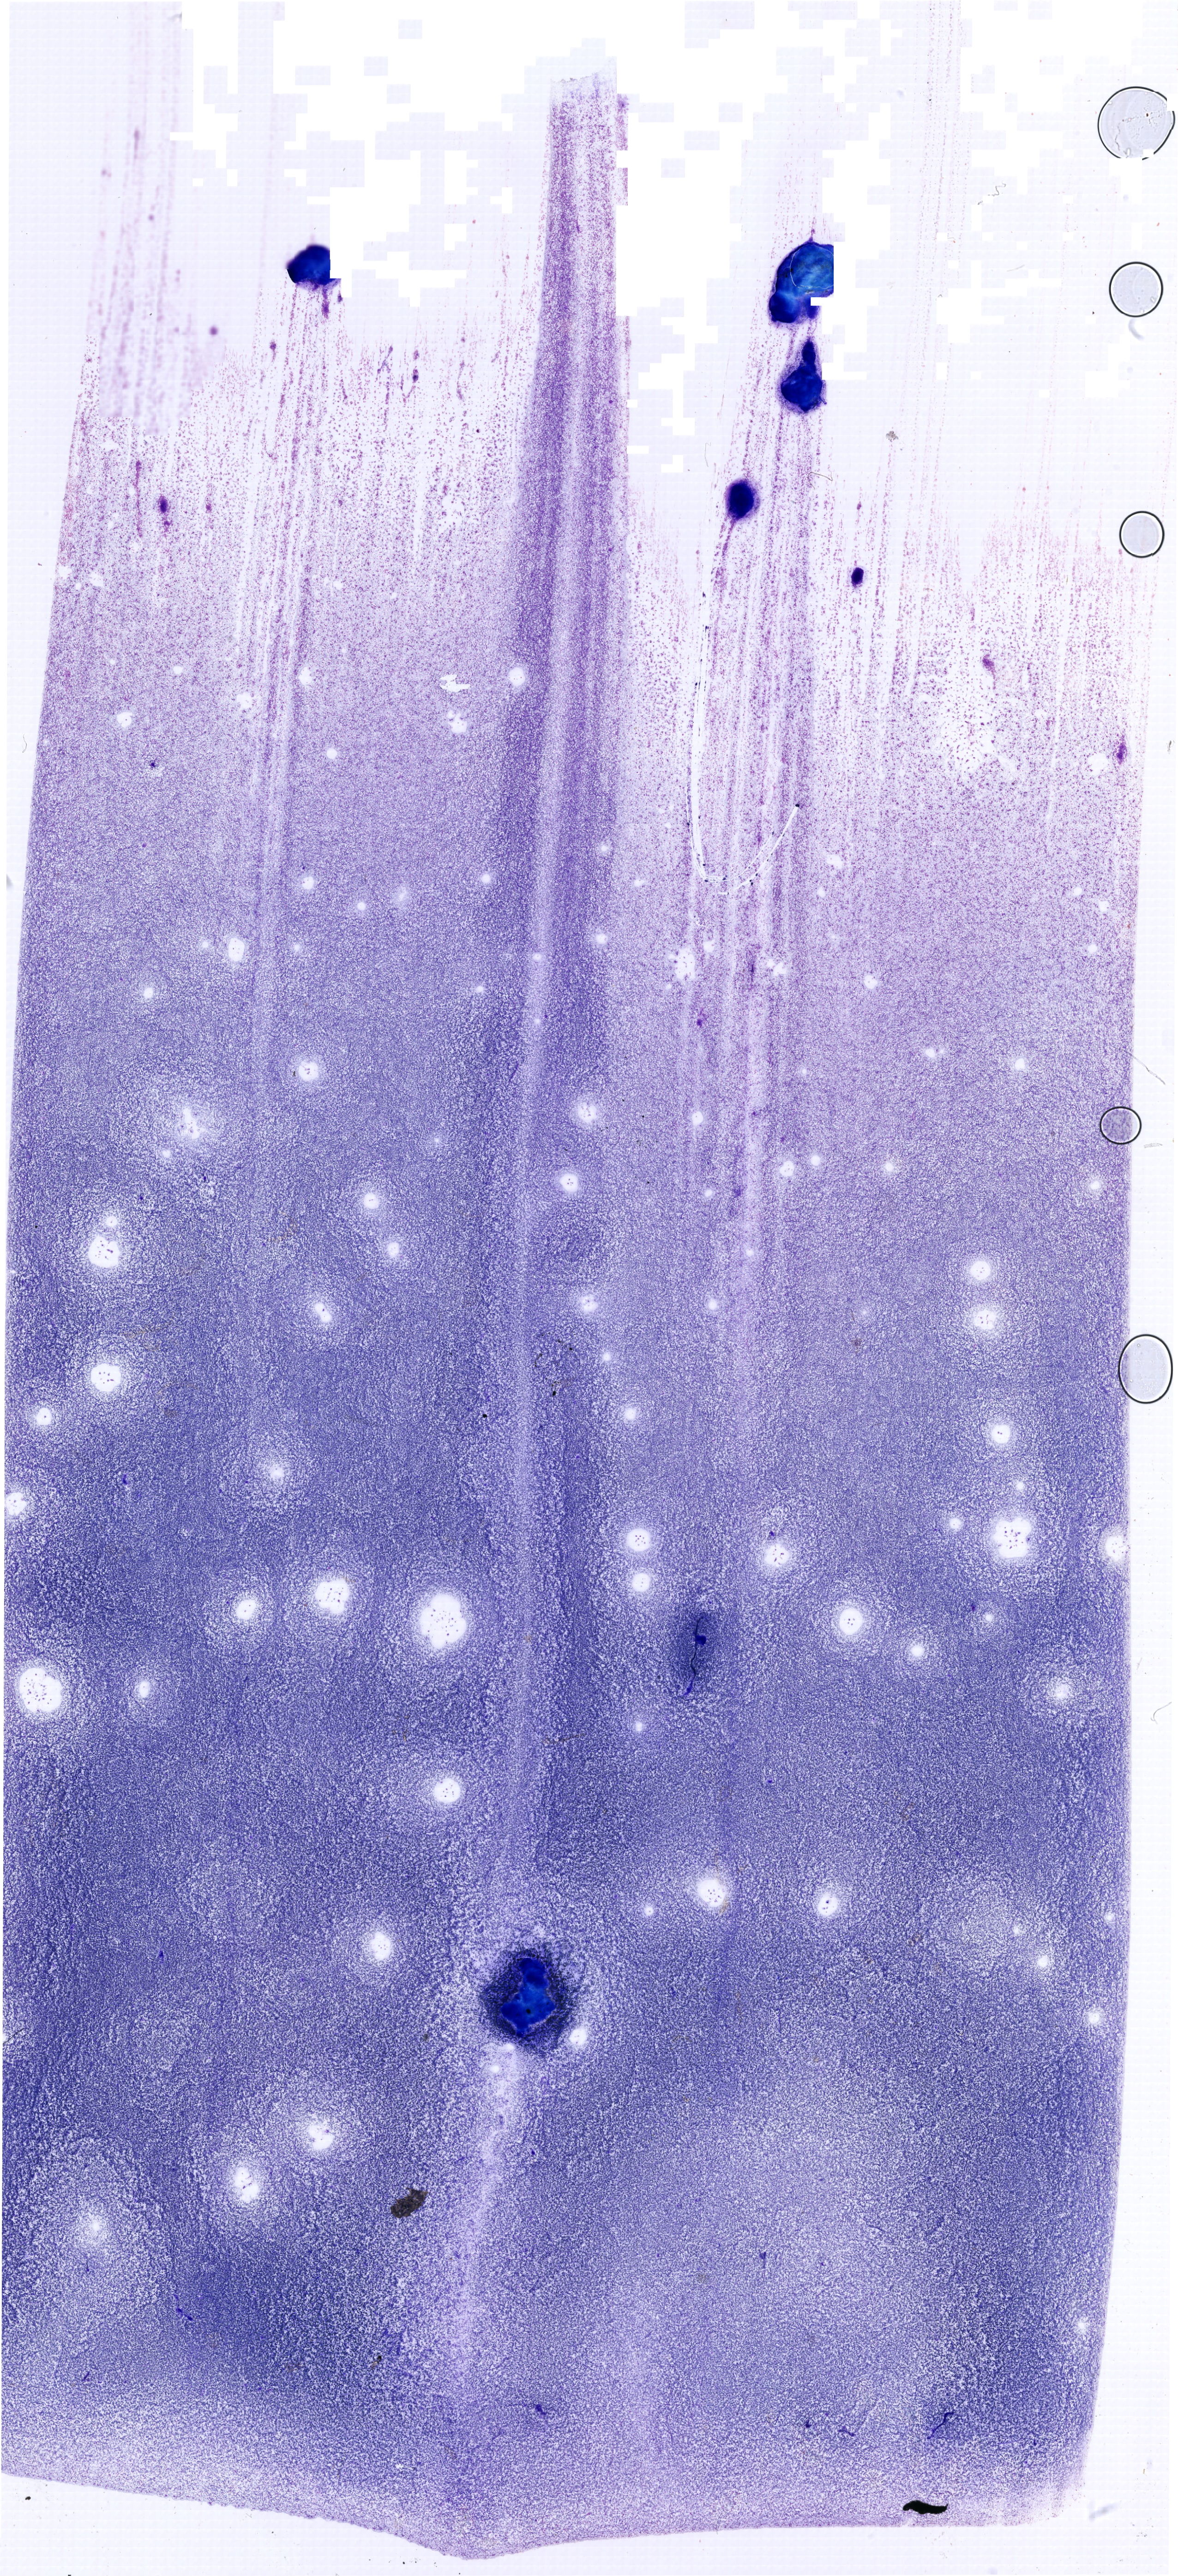
Whole-slide image of a May-Grünwald-Giemsa (MGG)-stained bone marrow aspirate smear, low-resolution overview of the scanned area, about 19.9 x 43.6 mm. Patient sex: male.
Diagnosis: Mixed Phenotype Acute Leukemia, B/Myeloid.